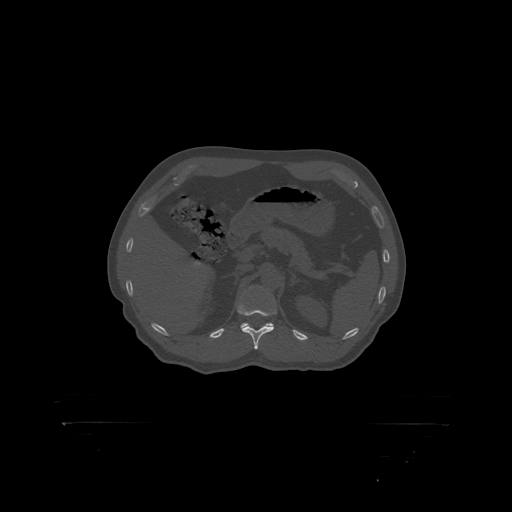
CT including the spine, one axial slice. Position 344 of 399 along the scan axis. Reconstruction kernel STANDARD. Bone window (W 1800 / L 400 HU). 1.25 mm slice thickness. 512 × 512 image matrix, field of view 650 × 650 mm. Patient: male, 46 years. From the clinical record (not read from this slice): primary cancer: skin.
Outlined on this slice (semi-automatic segmentation, software-assisted and operator-edited):
- T12 vertebra: bounding box (x1, y1, x2, y2) in pixels: (238, 297, 277, 316)